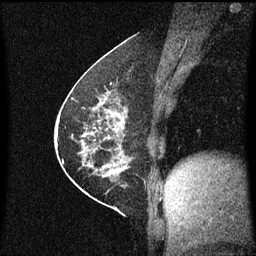
Breast MRI (dynamic contrast-enhanced), one sagittal slice. Slice 29 of 60 in the series (ordered by position). Dynamic contrast-enhanced series, image 2 of 3 at this slice position (ordered by acquisition). 1.5 T. TE 4.2 ms, TR 8.4 ms. 256 × 256 image matrix, field of view 200 × 200 mm. Patient: female, 60 years.
Annotated regions visible in this slice (semi-automatic segmentation, software-assisted and operator-edited):
- analysis volume of interest (the breast-tissue region the enhancement analysis was run in; not a lesion): box from (x=69, y=66) to (x=142, y=193) px
- tumour enhancement mask (voxels above the 70 % enhancement threshold inside the analysis volume of interest): (x=69, y=68)–(x=129, y=177)